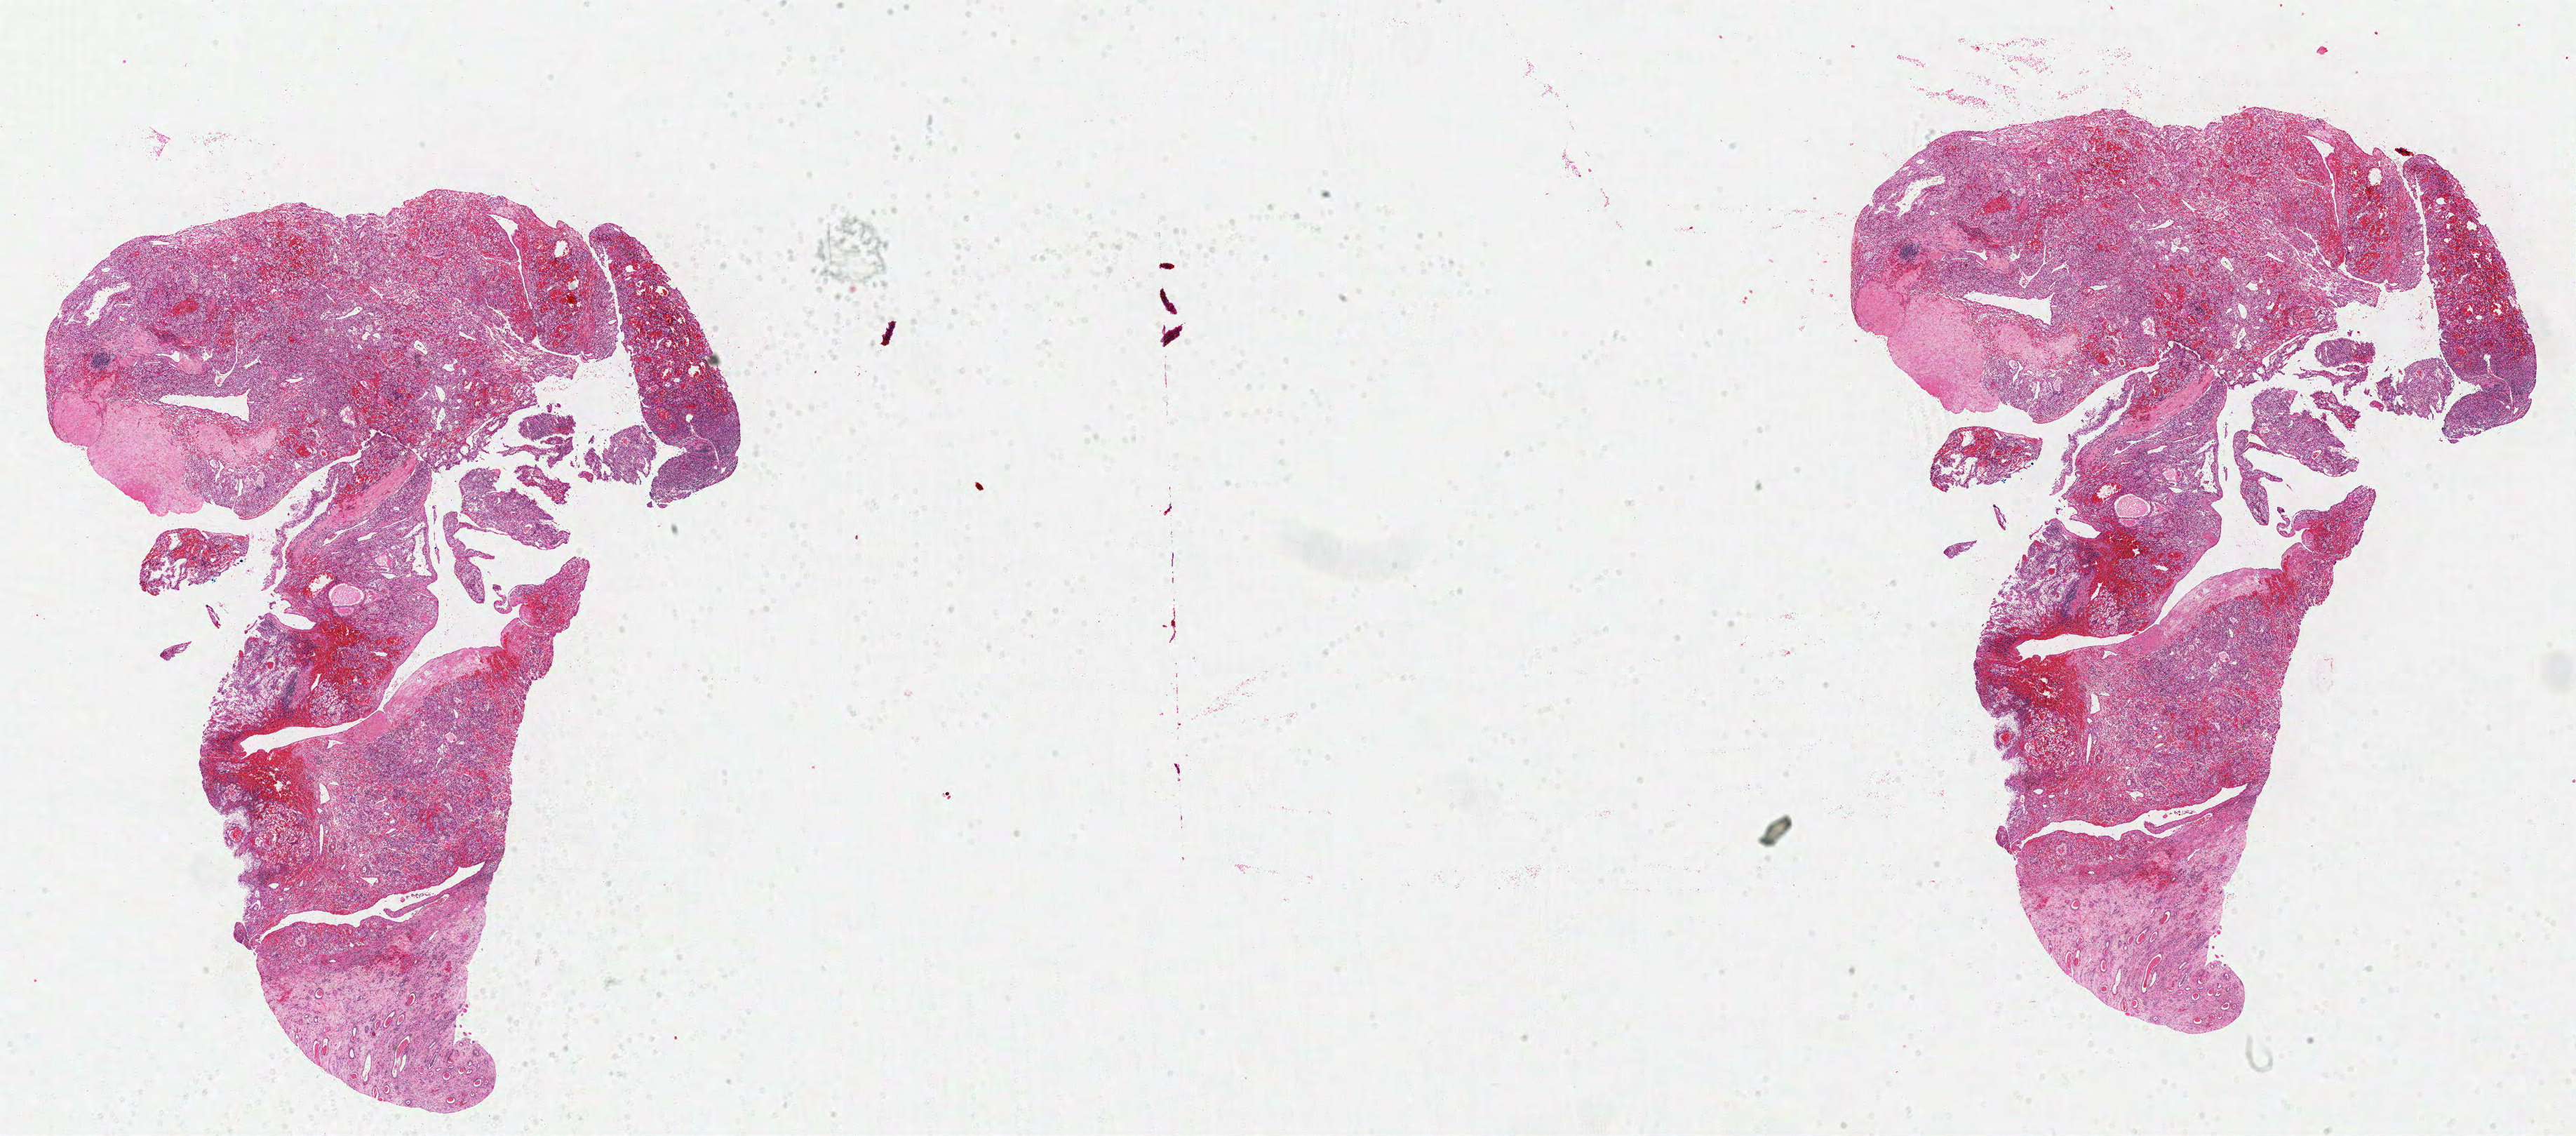
H&E whole-slide image — low-resolution overview of the scanned area, about 28.9 x 12.7 mm (slide scanned at 40x), formalin-fixed paraffin-embedded (FFPE) diagnostic section, primary tumour sample from the kidney. Female, age 67 years at initial diagnosis.
Diagnosis: Clear cell adenocarcinoma, NOS.